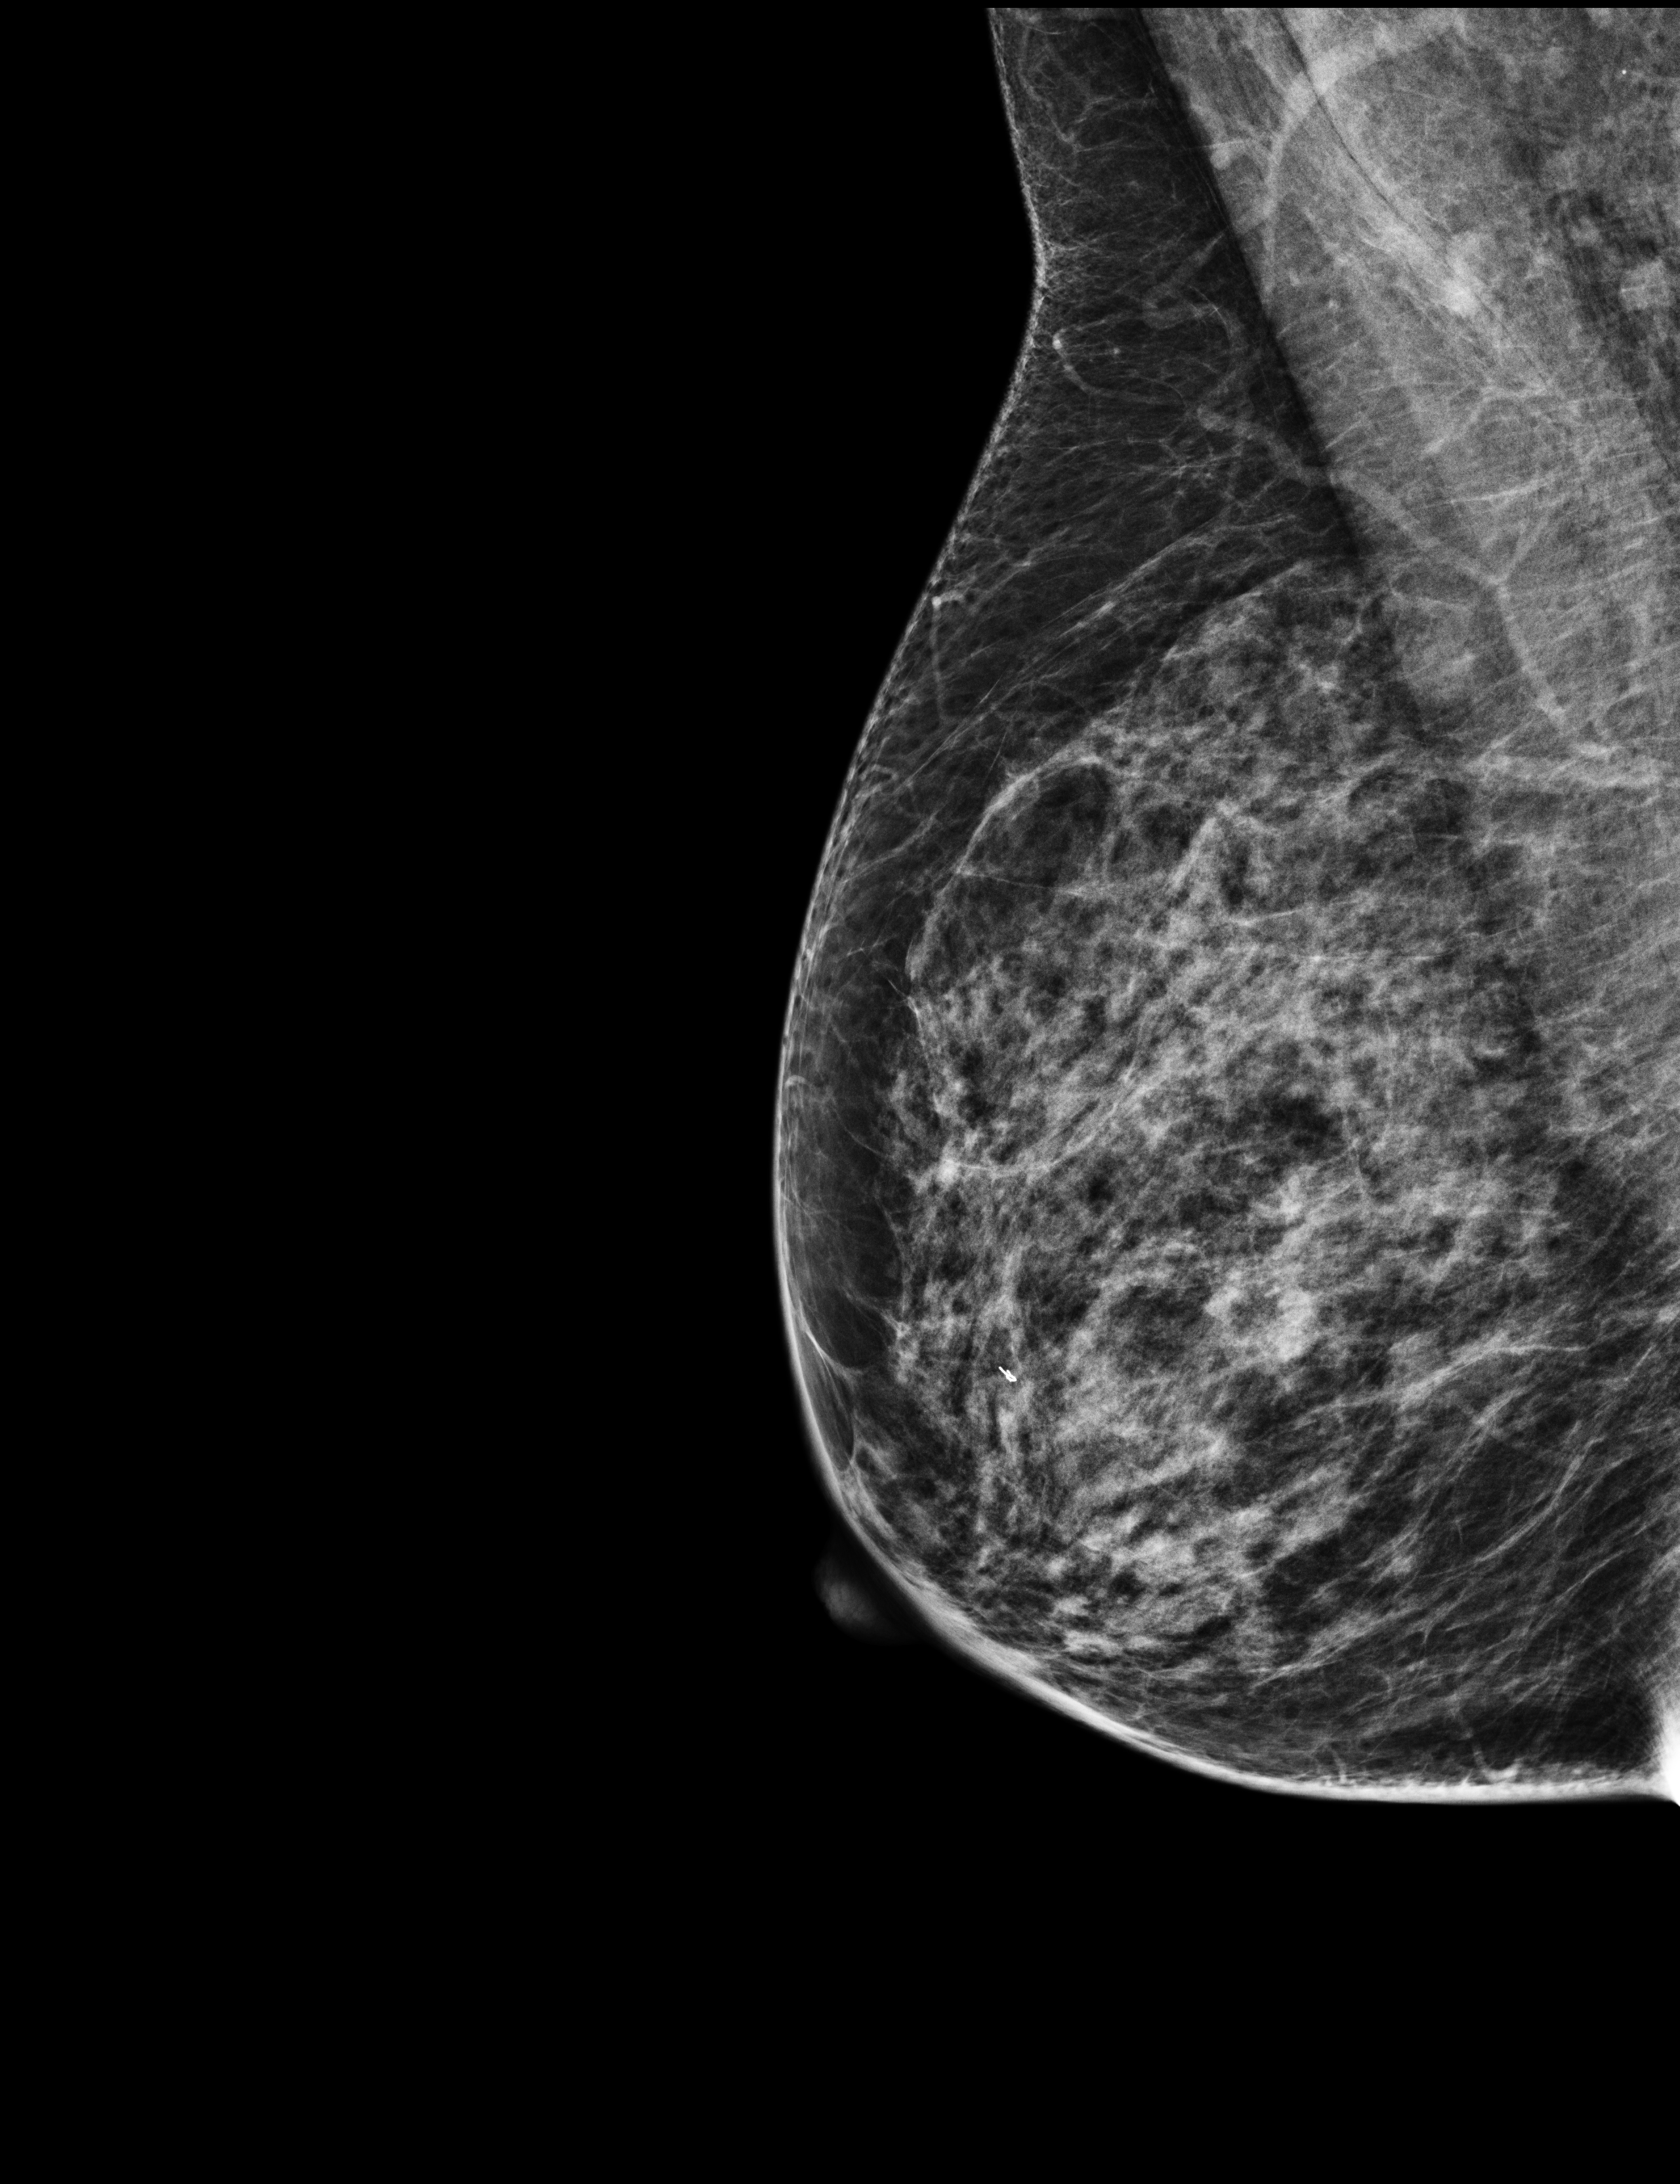
Screening examination; compressed breast thickness 54 mm; system: Selenia Dimensions. Patient aged 61 years (female).
Image type: full-field digital mammogram. Breast: right. Projection: mediolateral oblique (MLO) view.